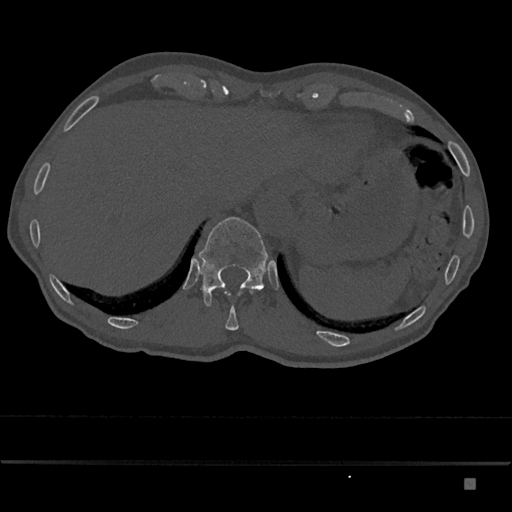
CT including the spine, one axial slice; position 638 of 797 along the scan axis; reconstruction kernel Br40s/3; bone window (W 1800 / L 400 HU); 0.5 mm slice thickness; 512 × 512 image matrix. Male patient, age 72 years. From the clinical record (not read from this slice): primary cancer: prostate.
Annotated regions visible in this slice (semi-automatic segmentation, software-assisted and operator-edited):
- T11 vertebra: bounding box (x1, y1, x2, y2) in pixels: (225, 291, 252, 330)
- T12 vertebra: (199, 217, 268, 306)